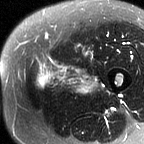
MRI of an extremity soft-tissue mass, one axial slice; position 18 of 60 along the scan axis; T2-weighted fat-saturated; MR volume resampled by the dataset authors to the PET/CT grid (not the native acquisition matrix); 3.27 mm slice thickness; 144 × 144 image matrix, field of view 141 × 141 mm. Female patient. From the clinical record (not read from this slice): histological type: pleiomorphic leiomyosarcoma; grade: intermediate; site of the primary tumour: left thigh.
Annotated regions visible in this slice (expert contour drawn on MRI and transferred to this co-registered scan by the dataset authors):
- gross tumour volume including surrounding oedema: bounding box (x1, y1, x2, y2) in pixels: (36, 56, 101, 95)